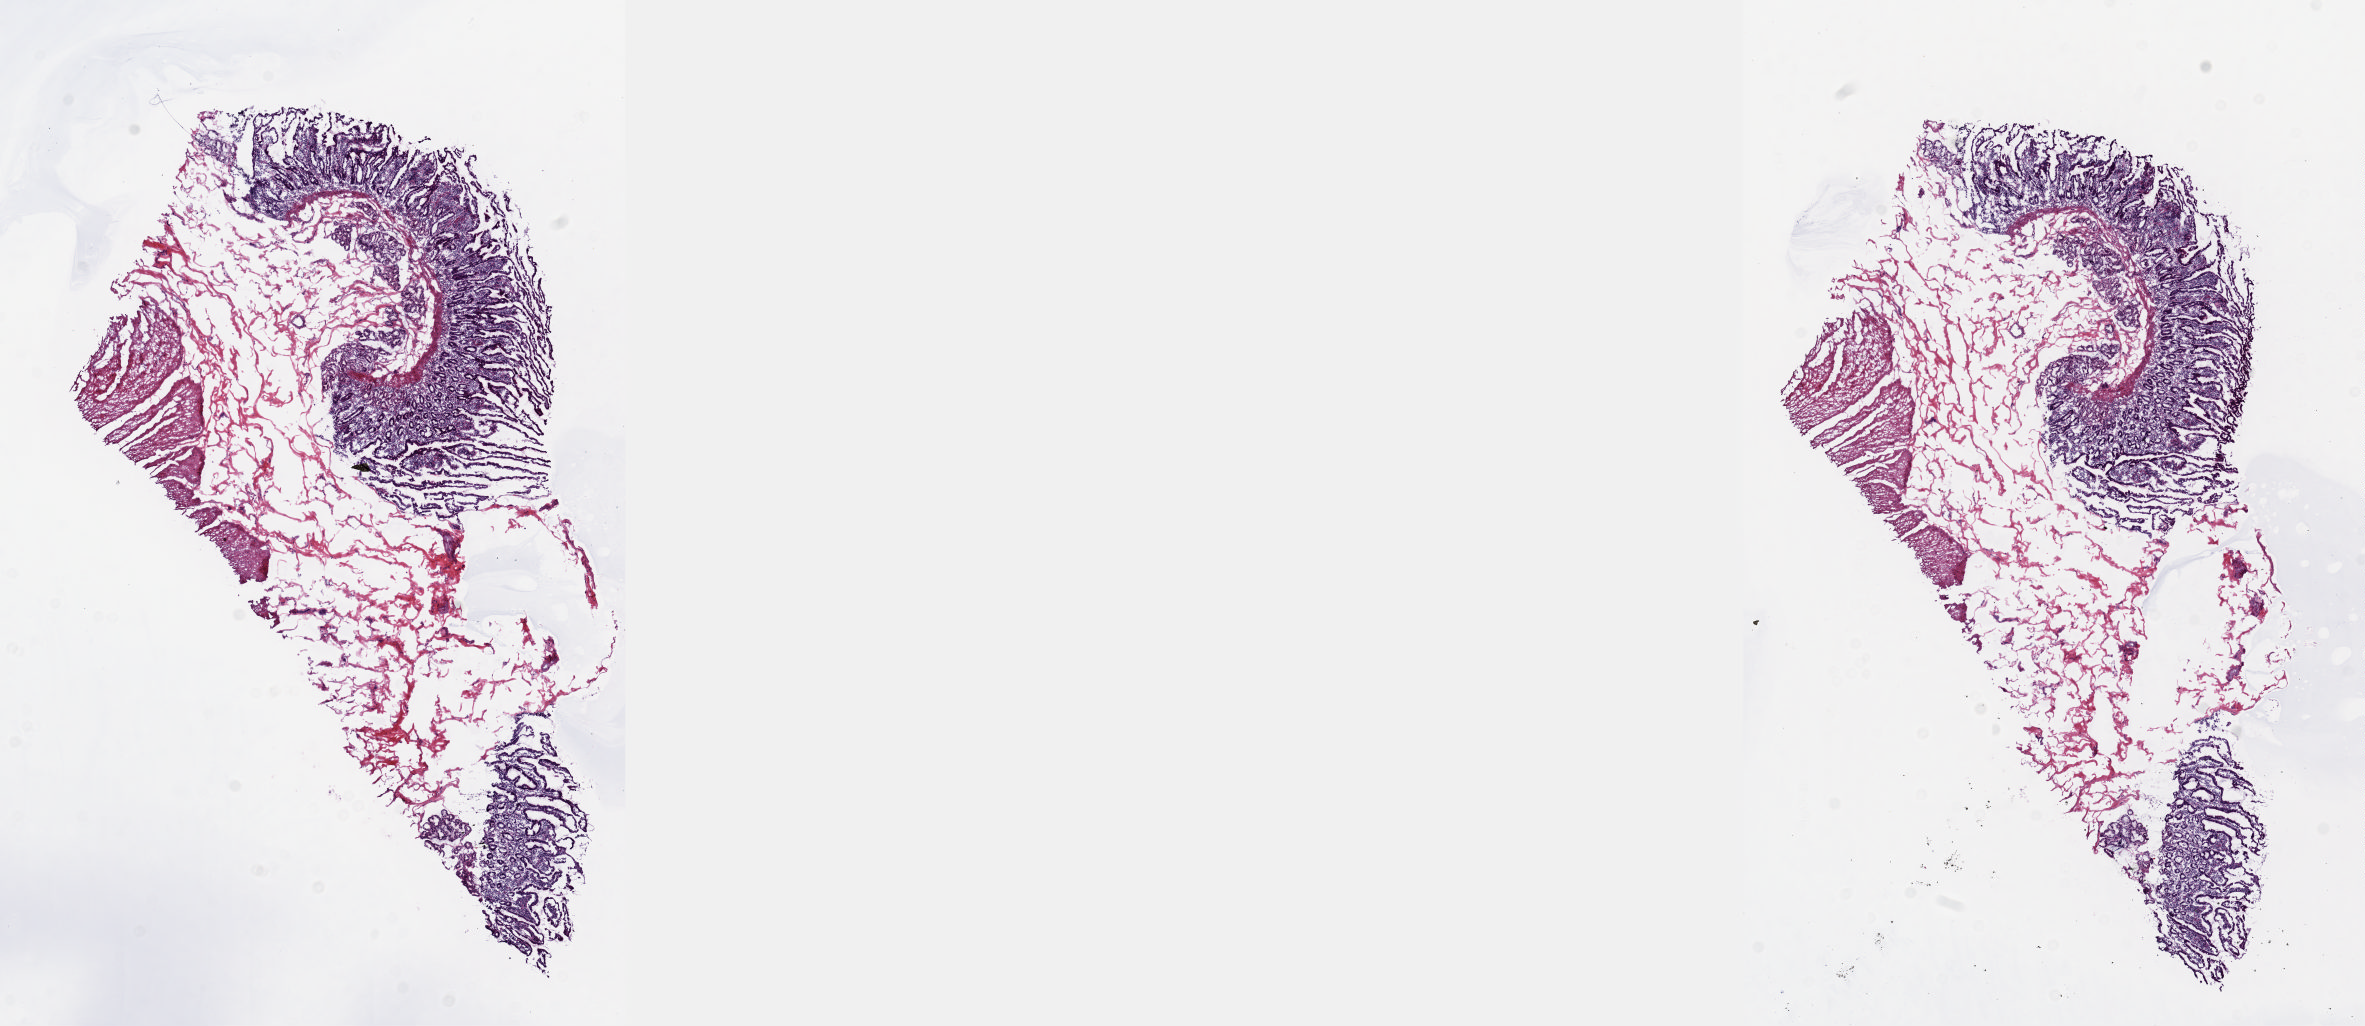
Digitized H&E-stained tissue section (whole slide) — shown as a low-resolution overview of the whole scanned area (about 19.1 x 8.3 mm); frozen section from the top of the tissue portion; sample: solid tissue normal (non-tumour tissue), pancreas. Male patient; age at initial diagnosis 71 years. Slide review estimates, as recorded: tumour cells 0%, tumour nuclei 0%, normal cells 60%, stromal cells 40%, necrosis 0%. Infiltration values recorded for this section: lymphocyte infiltration 4%, monocyte infiltration 2%, neutrophil infiltration 6%.
This section: solid tissue normal (non-tumour) sample from the same patient. Patient diagnosis: Infiltrating duct carcinoma, NOS (head of pancreas).